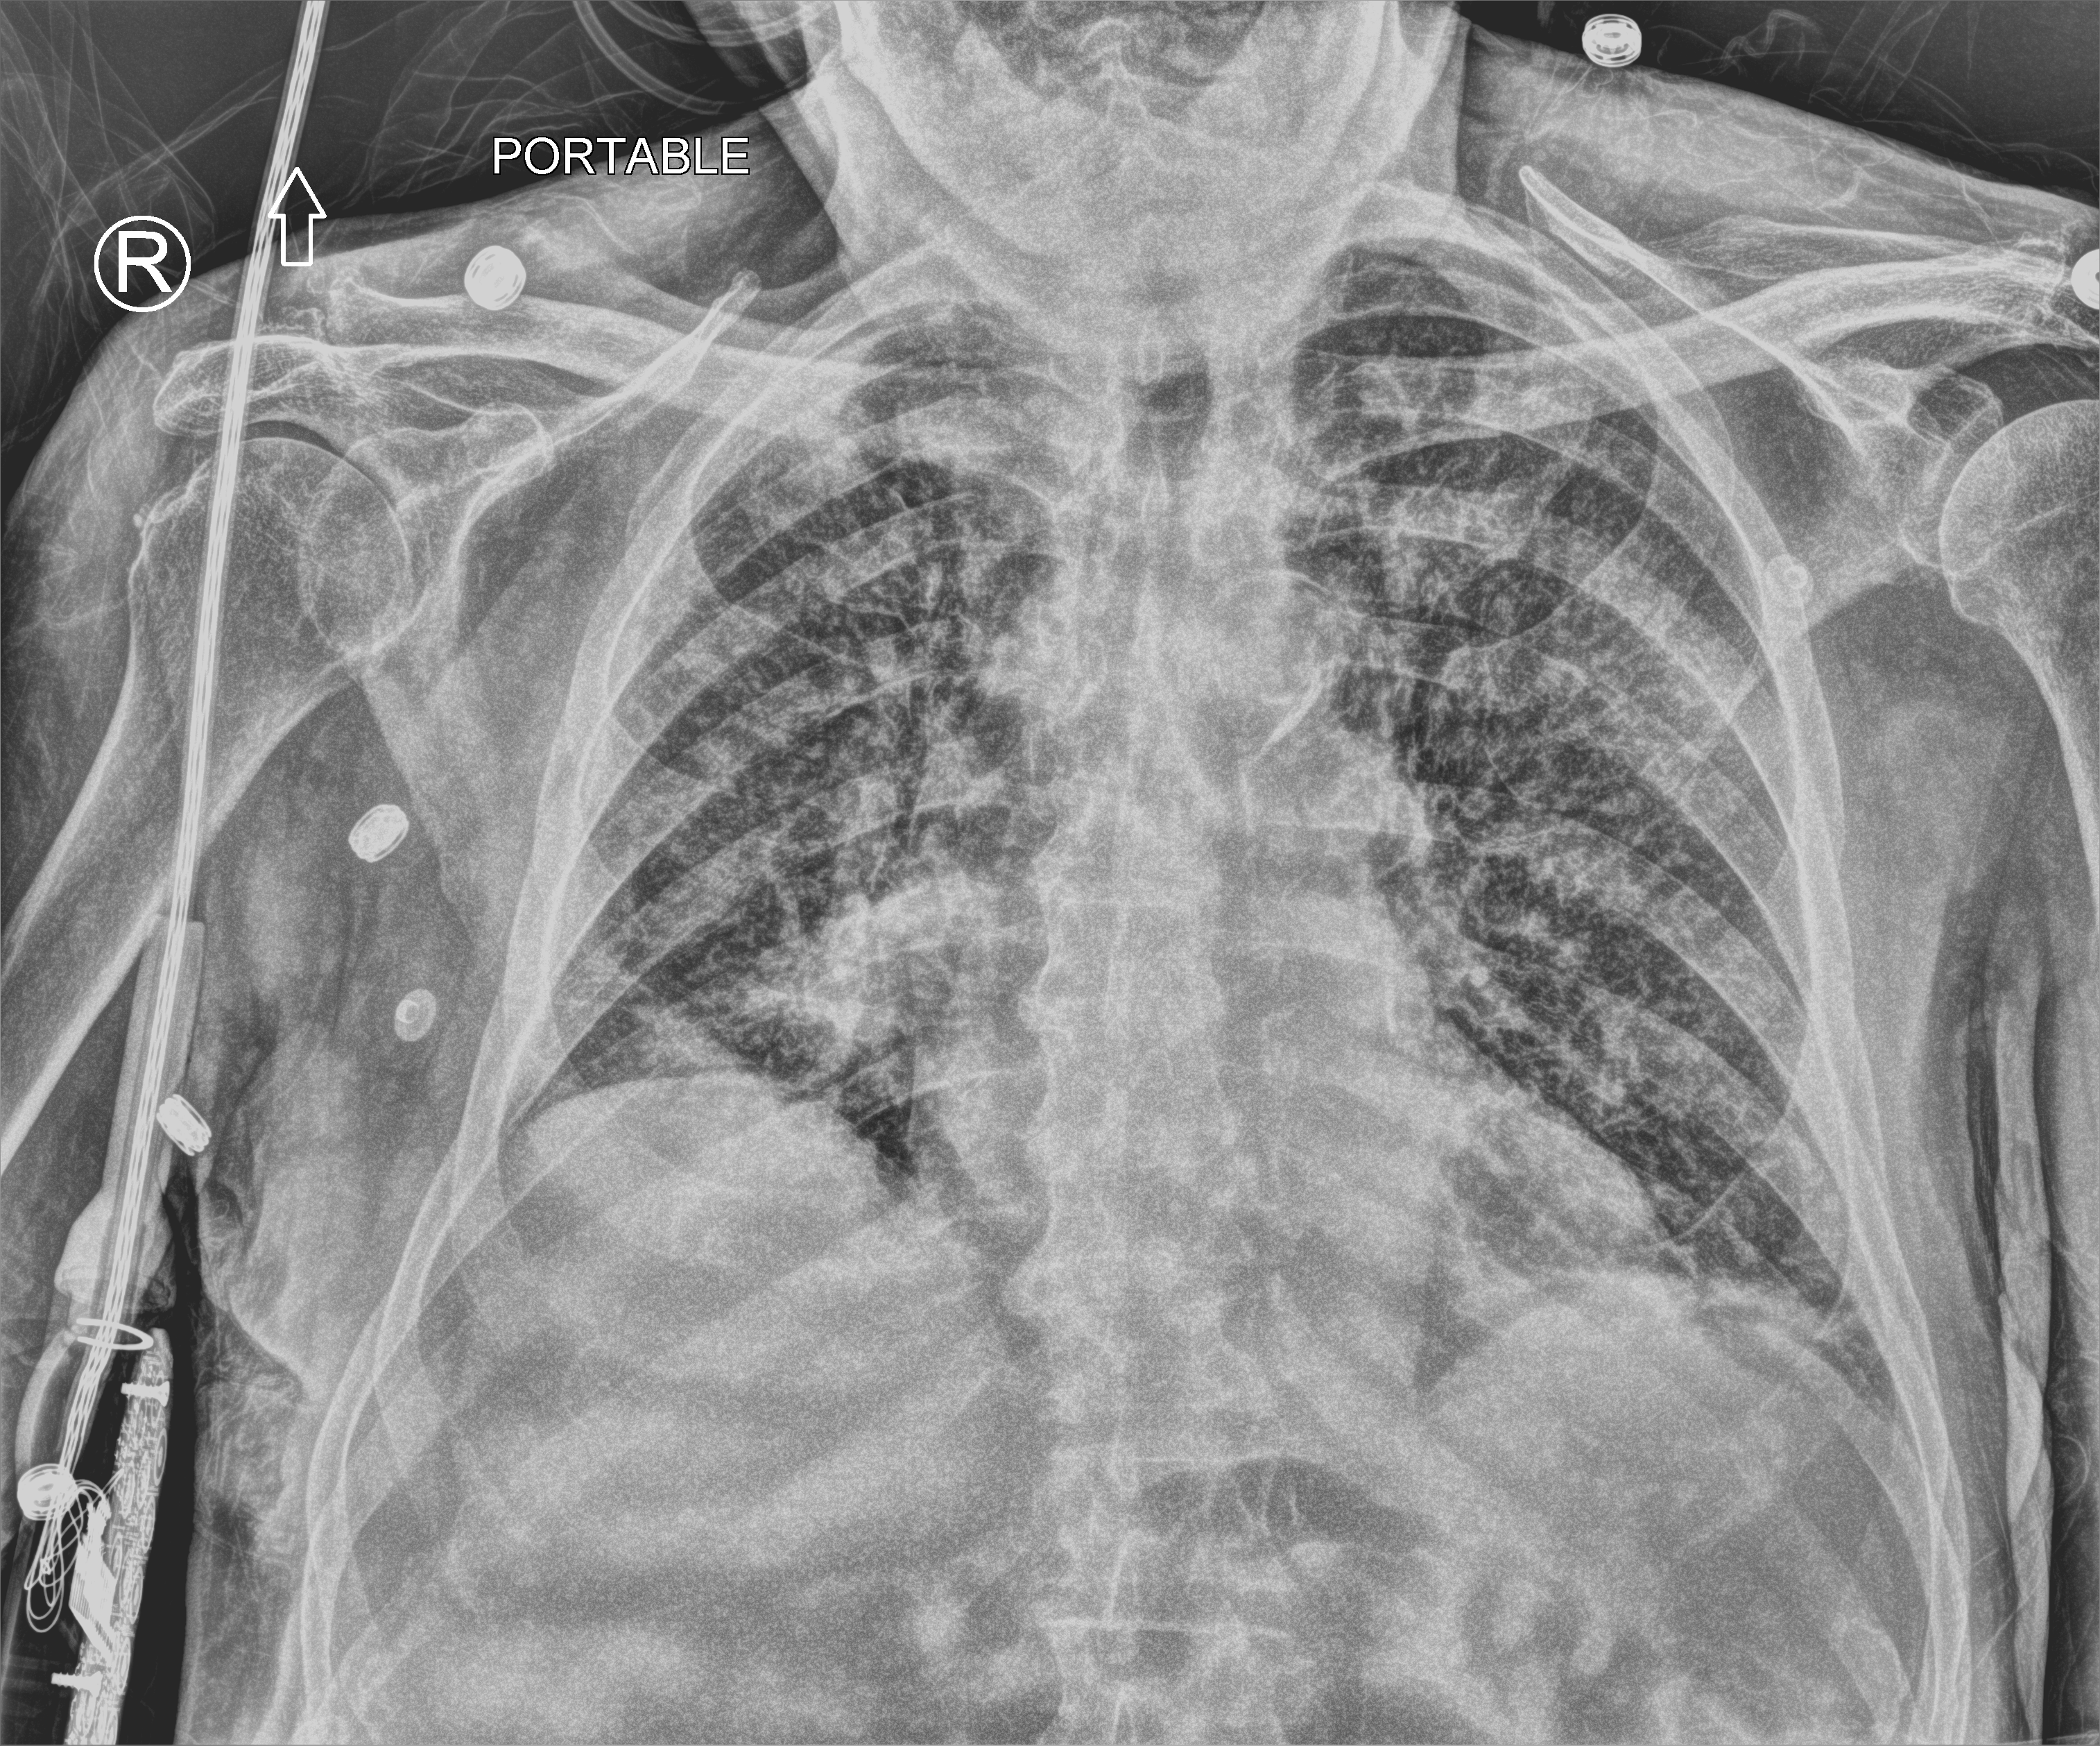
Chest X-ray (portable), anteroposterior (AP) projection. Patient hospitalised with COVID-19; male, aged 75–90 years.
Admission-level facts for this patient (not findings on this image; timing relative to this image not recorded): mechanically ventilated during this hospital stay: yes.